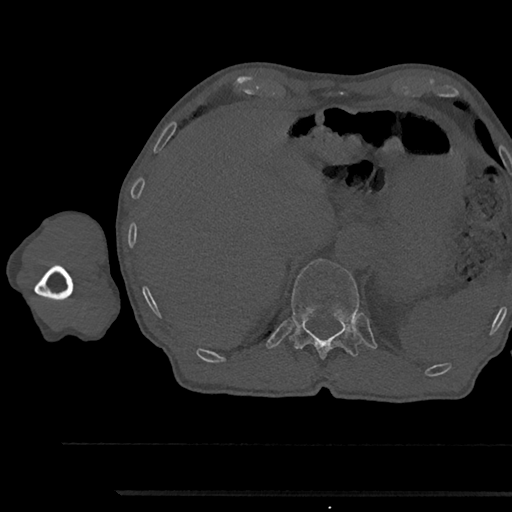
CT including the spine, one axial slice; position 717 of 797 along the scan axis; reconstruction kernel Br40s/3; bone window (W 1800 / L 400 HU); 0.5 mm slice thickness; 512 × 512 image matrix, field of view 367 × 367 mm. Male patient, age 79 years. From the clinical record (not read from this slice): primary cancer: prostate.
Structures marked on this image (semi-automatic segmentation, software-assisted and operator-edited):
- T12 vertebra: bounding box (x1, y1, x2, y2) in pixels: (291, 258, 361, 360)